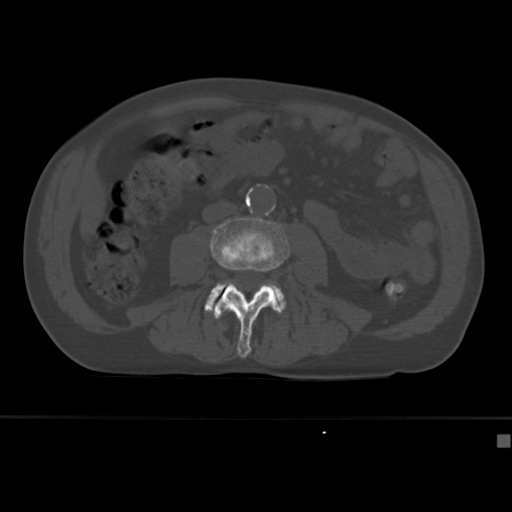
CT including the spine, one axial slice. Position 121 of 430 along the scan axis. Bone window (W 1800 / L 400 HU). 512 × 512 image matrix, field of view 337 × 337 mm. Male patient, age 64 years. From the clinical record (not read from this slice): primary cancer: uterus.
Outlined on this slice (semi-automatic segmentation, software-assisted and operator-edited):
- L3 vertebra: box from (x=210, y=217) to (x=290, y=358) px
- L4 vertebra: (x=204, y=282)–(x=286, y=313)